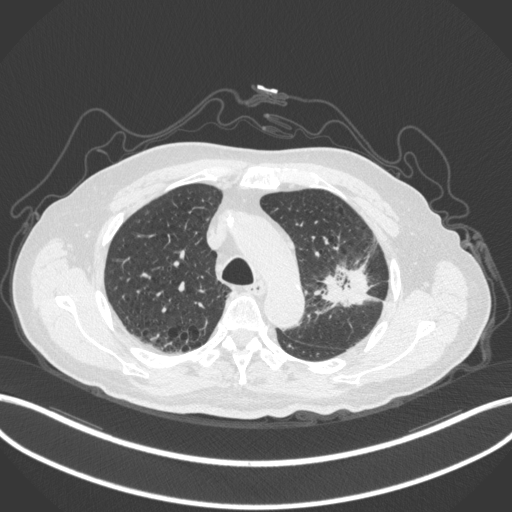
Chest CT, one axial slice. Position 217 of 331 along the scan axis. Reconstruction kernel B31f. Lung window (W 1500 / L -600 HU). 512 × 512 image matrix, field of view 400 × 400 mm. Patient: male, 79 years. Case-level facts recorded for this patient, not image findings: clinical TNM (as recorded): T2a N1 M1; histopathological grade: G3.
Outlined on this slice (rectangle marked by the reading radiologist):
- lung tumour (recorded histology: adenocarcinoma): bounding box [x1, y1, x2, y2] px = [322, 266, 376, 310]